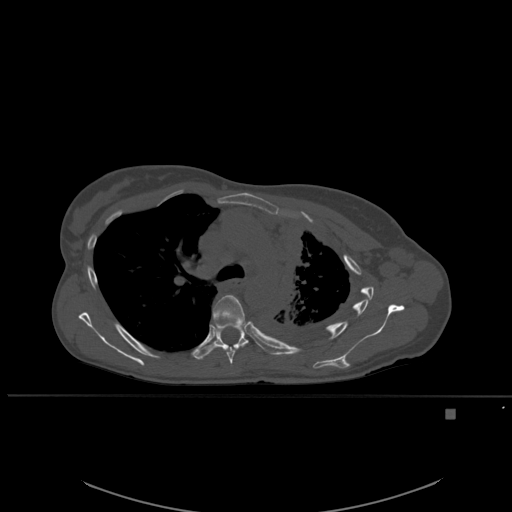
CT including the spine, one axial slice; slice 391 of 537 in the series (ordered by position); bone window (W 1800 / L 400 HU); 1.5 mm slice thickness; 512 × 512 image matrix, field of view 440 × 440 mm. Patient: female, 45 years. Case-level facts recorded for this patient, not image findings: primary cancer: lung.
Annotated regions visible in this slice (semi-automatic segmentation, software-assisted and operator-edited):
- T5 vertebra: box from (x=213, y=295) to (x=247, y=366) px
- T6 vertebra: (x=196, y=321)–(x=265, y=361)